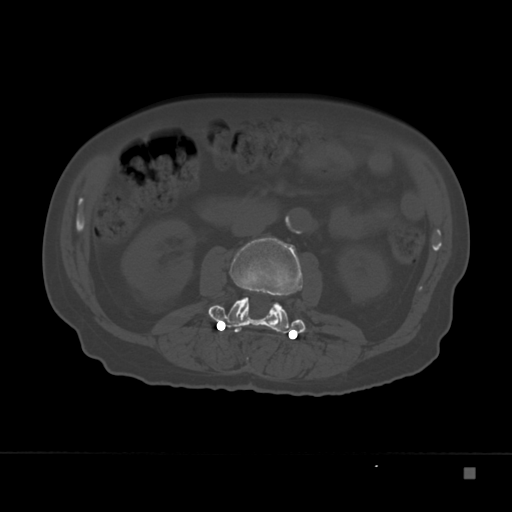
CT including the spine, one axial slice. Position 81 of 332 along the scan axis. Bone window (W 1800 / L 400 HU). 1.5 mm slice thickness. 512 × 512 image matrix, field of view 389 × 389 mm. Patient: male, 72 years. Case-level facts recorded for this patient, not image findings: primary cancer: skeletal.
Structures marked on this image (semi-automatically segmented with operator editing):
- L2 vertebra: bounding box <230,237,303,327> (left, top, right, bottom; pixels)
- L3 vertebra: <208,295,306,334>